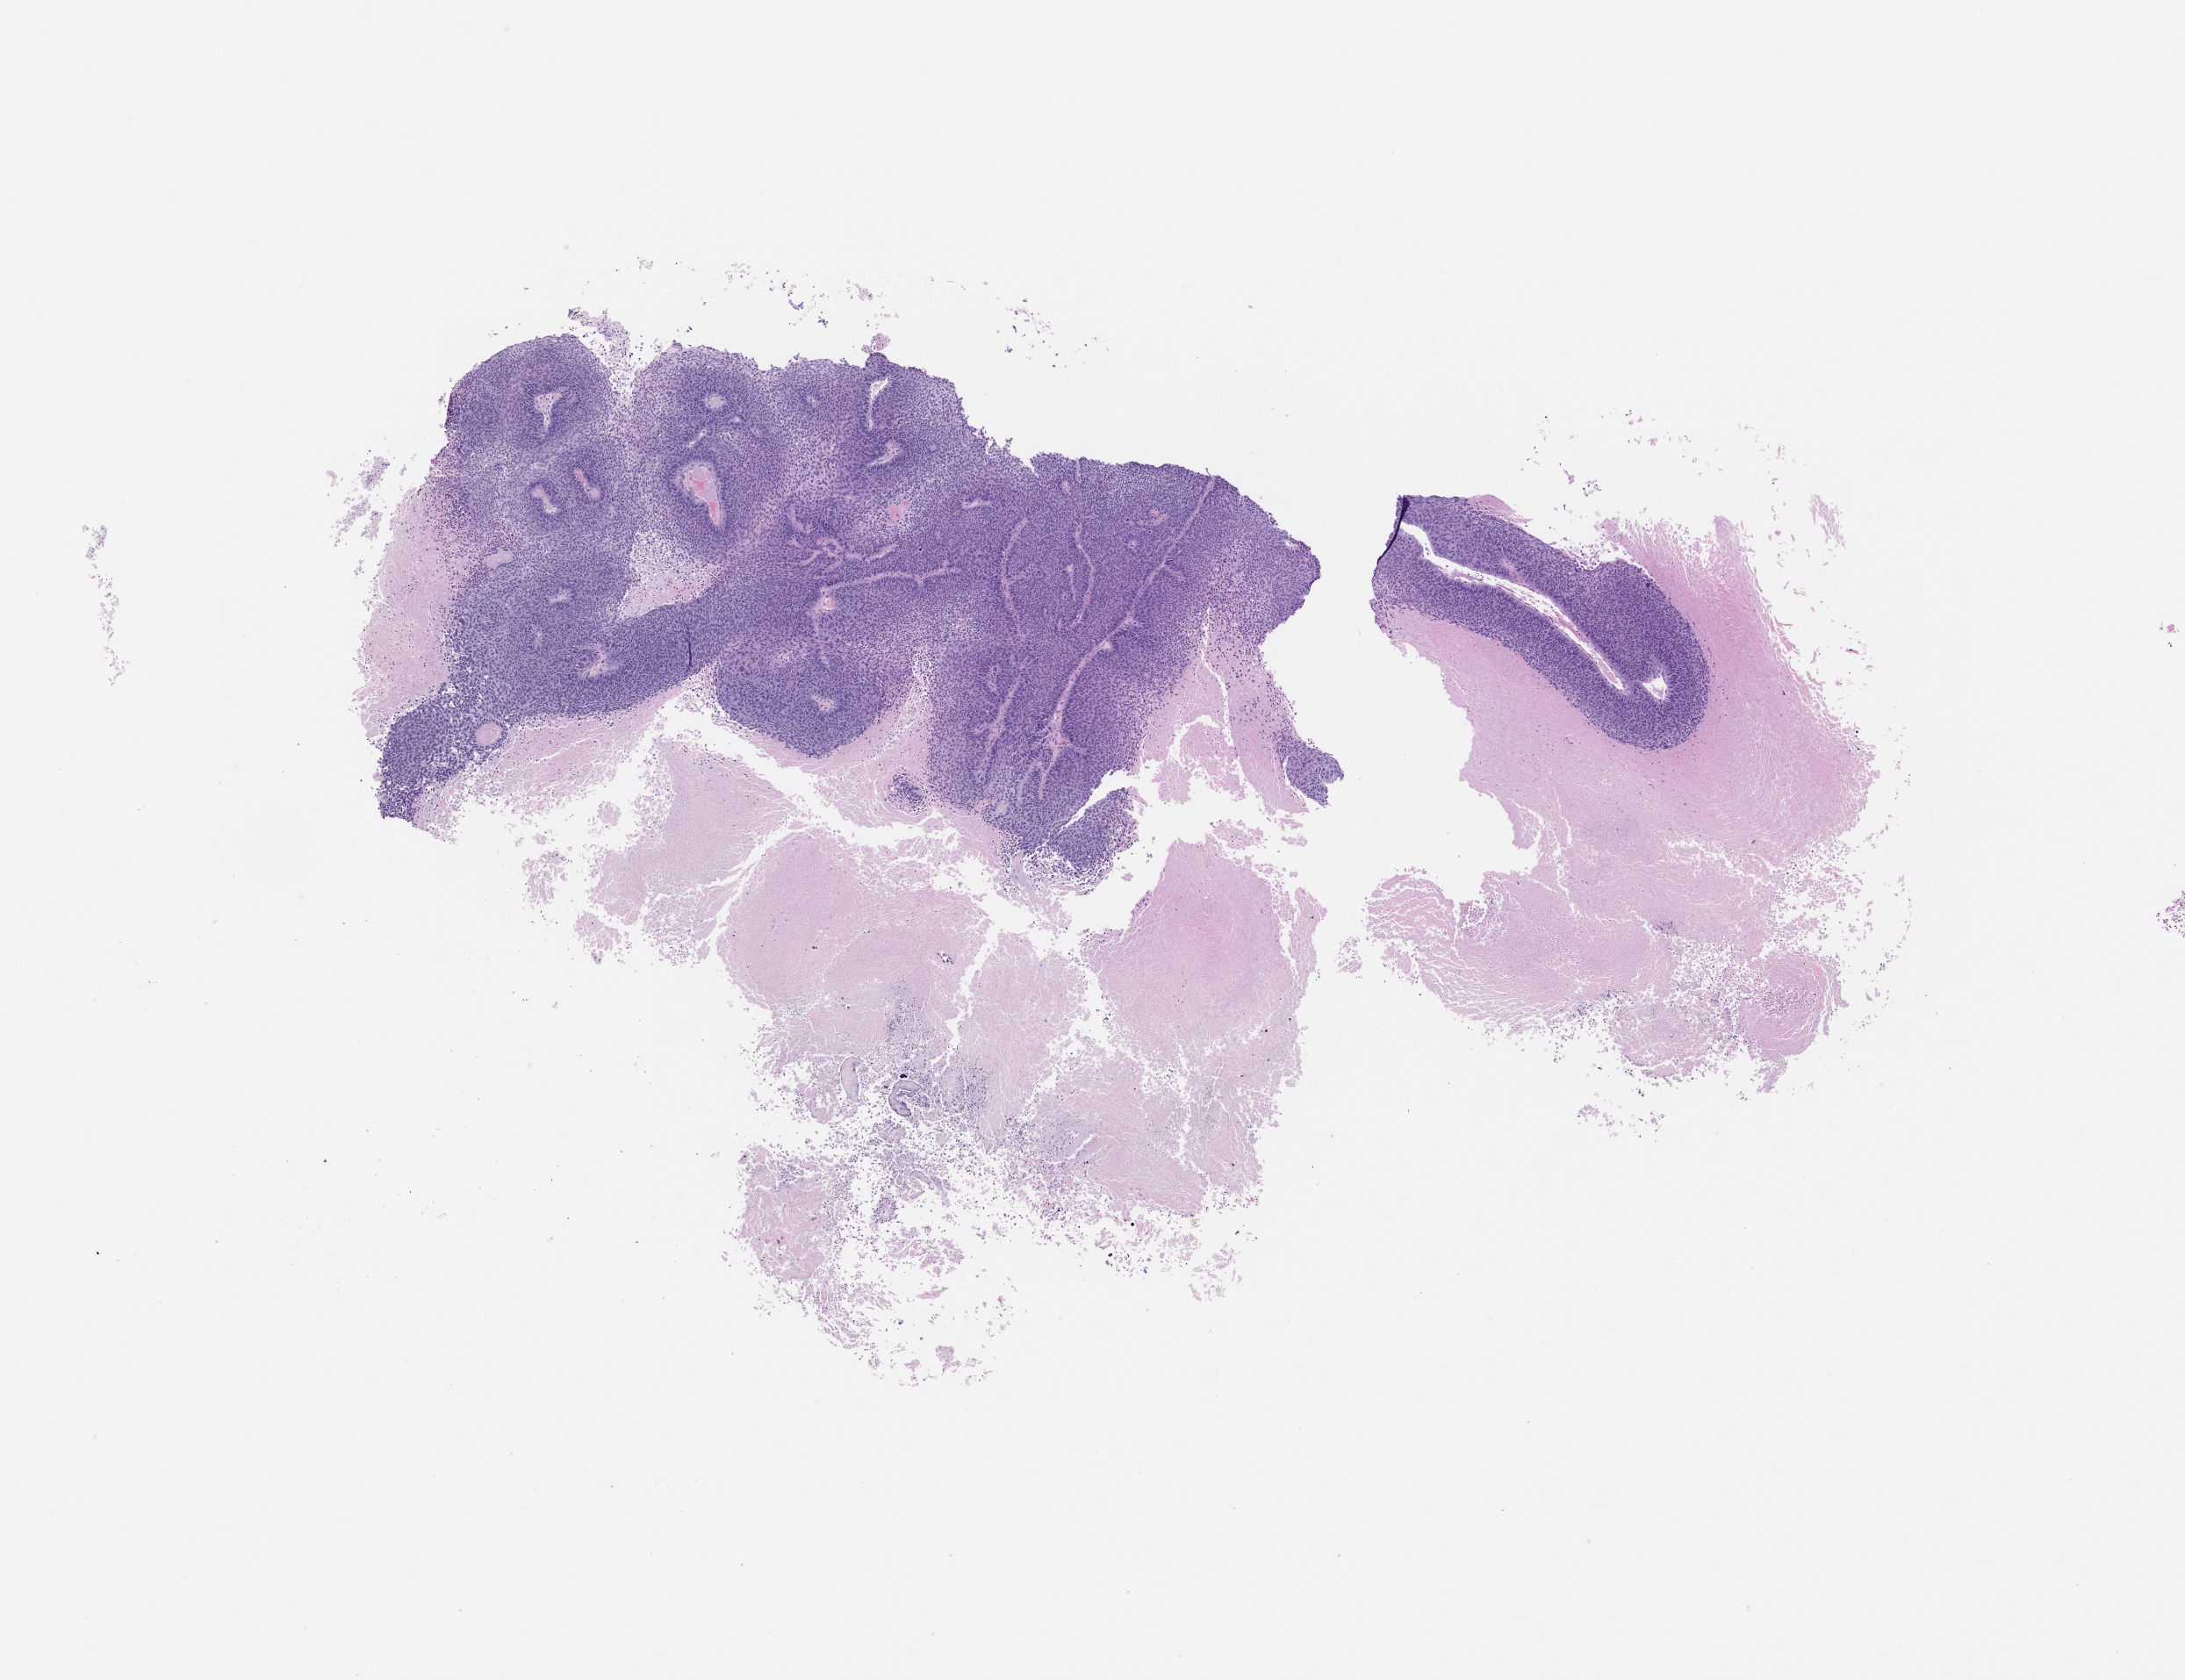
Whole-slide image, hematoxylin and eosin (H&E): patient-derived xenograft (human tumor grown in a mouse) — shown as a low-resolution overview of the whole scanned area (about 10.0 x 7.7 mm), FFPE section, tumor site category: lung.
- originating patient diagnosis: Lung Squamous Cell Carcinoma